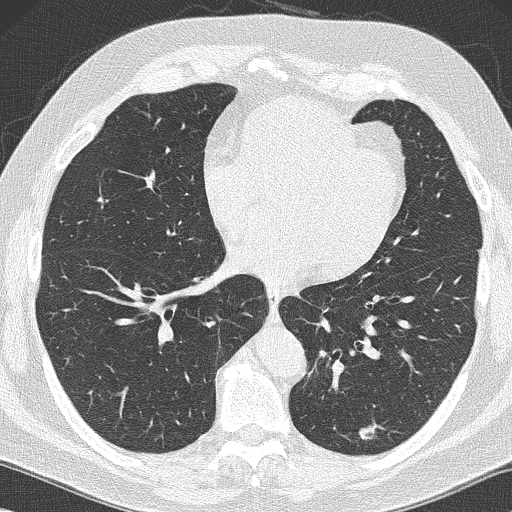
Chest CT (low-dose screening protocol), one axial image; first (baseline) screen; lung window (W 1500 / L -600 HU); lung (sharp) reconstruction kernel (B50f); 512 × 512 image matrix. Male participant, aged 59 years at enrolment. Former smoker at enrolment.
Expert-annotated lung lesion, bounding box [x1, y1, x2, y2] px = [346, 414, 389, 452]. The screening reader recorded 2 non-calcified nodules or masses ≥4 mm on this exam; which of them this box marks is not recorded. Lung cancer was diagnosed 61 days after this screen: large cell carcinoma, NOS, left lower lobe, poorly differentiated (G3), stage IA (AJCC 6th edition), 14 mm at pathology.